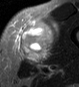
MRI of an extremity soft-tissue mass, one axial slice; position 27 of 45 along the scan axis; STIR; MR volume resampled by the dataset authors to the PET/CT grid (not the native acquisition matrix); 3.27 mm slice thickness; 79 × 87 image matrix. Male patient. From the clinical record (not read from this slice): histological type: pleiomorphic leiomyosarcoma; grade: high; site of the primary tumour: left thigh.
Outlined on this slice (expert contour drawn on MRI and transferred to this co-registered scan by the dataset authors):
- gross tumour volume including surrounding oedema: bounding box <18,18,58,63> (left, top, right, bottom; pixels)
- gross tumour volume (mass): <20,21,53,60>